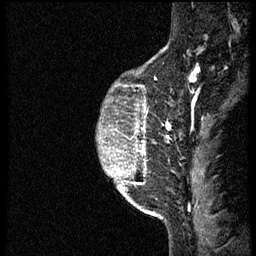
Breast MRI (dynamic contrast-enhanced), one sagittal slice; slice 47 of 56 in the series (ordered by position); dynamic contrast-enhanced study with each time point stored as its own series, time point 2 of 3 at this slice position (early post-contrast, ordered by acquisition time); 1.5 T; TE 4.2 ms, TR 21.3 ms; 2 mm slice thickness; 256 × 256 image matrix, field of view 200 × 200 mm. Patient: female, 41 years. Case-level facts recorded for this patient, not image findings: setting: breast cancer imaged before/during neoadjuvant chemotherapy; receptor status: HER2-positive.
Annotated regions visible in this slice (semi-automatic segmentation, software-assisted and operator-edited):
- analysis volume of interest (the breast-tissue region the enhancement analysis was run in; not a lesion): bounding box <122,73,176,205> (left, top, right, bottom; pixels)
- tumour enhancement mask (voxels above the 100 % enhancement threshold inside the analysis volume of interest): <140,122,171,153>